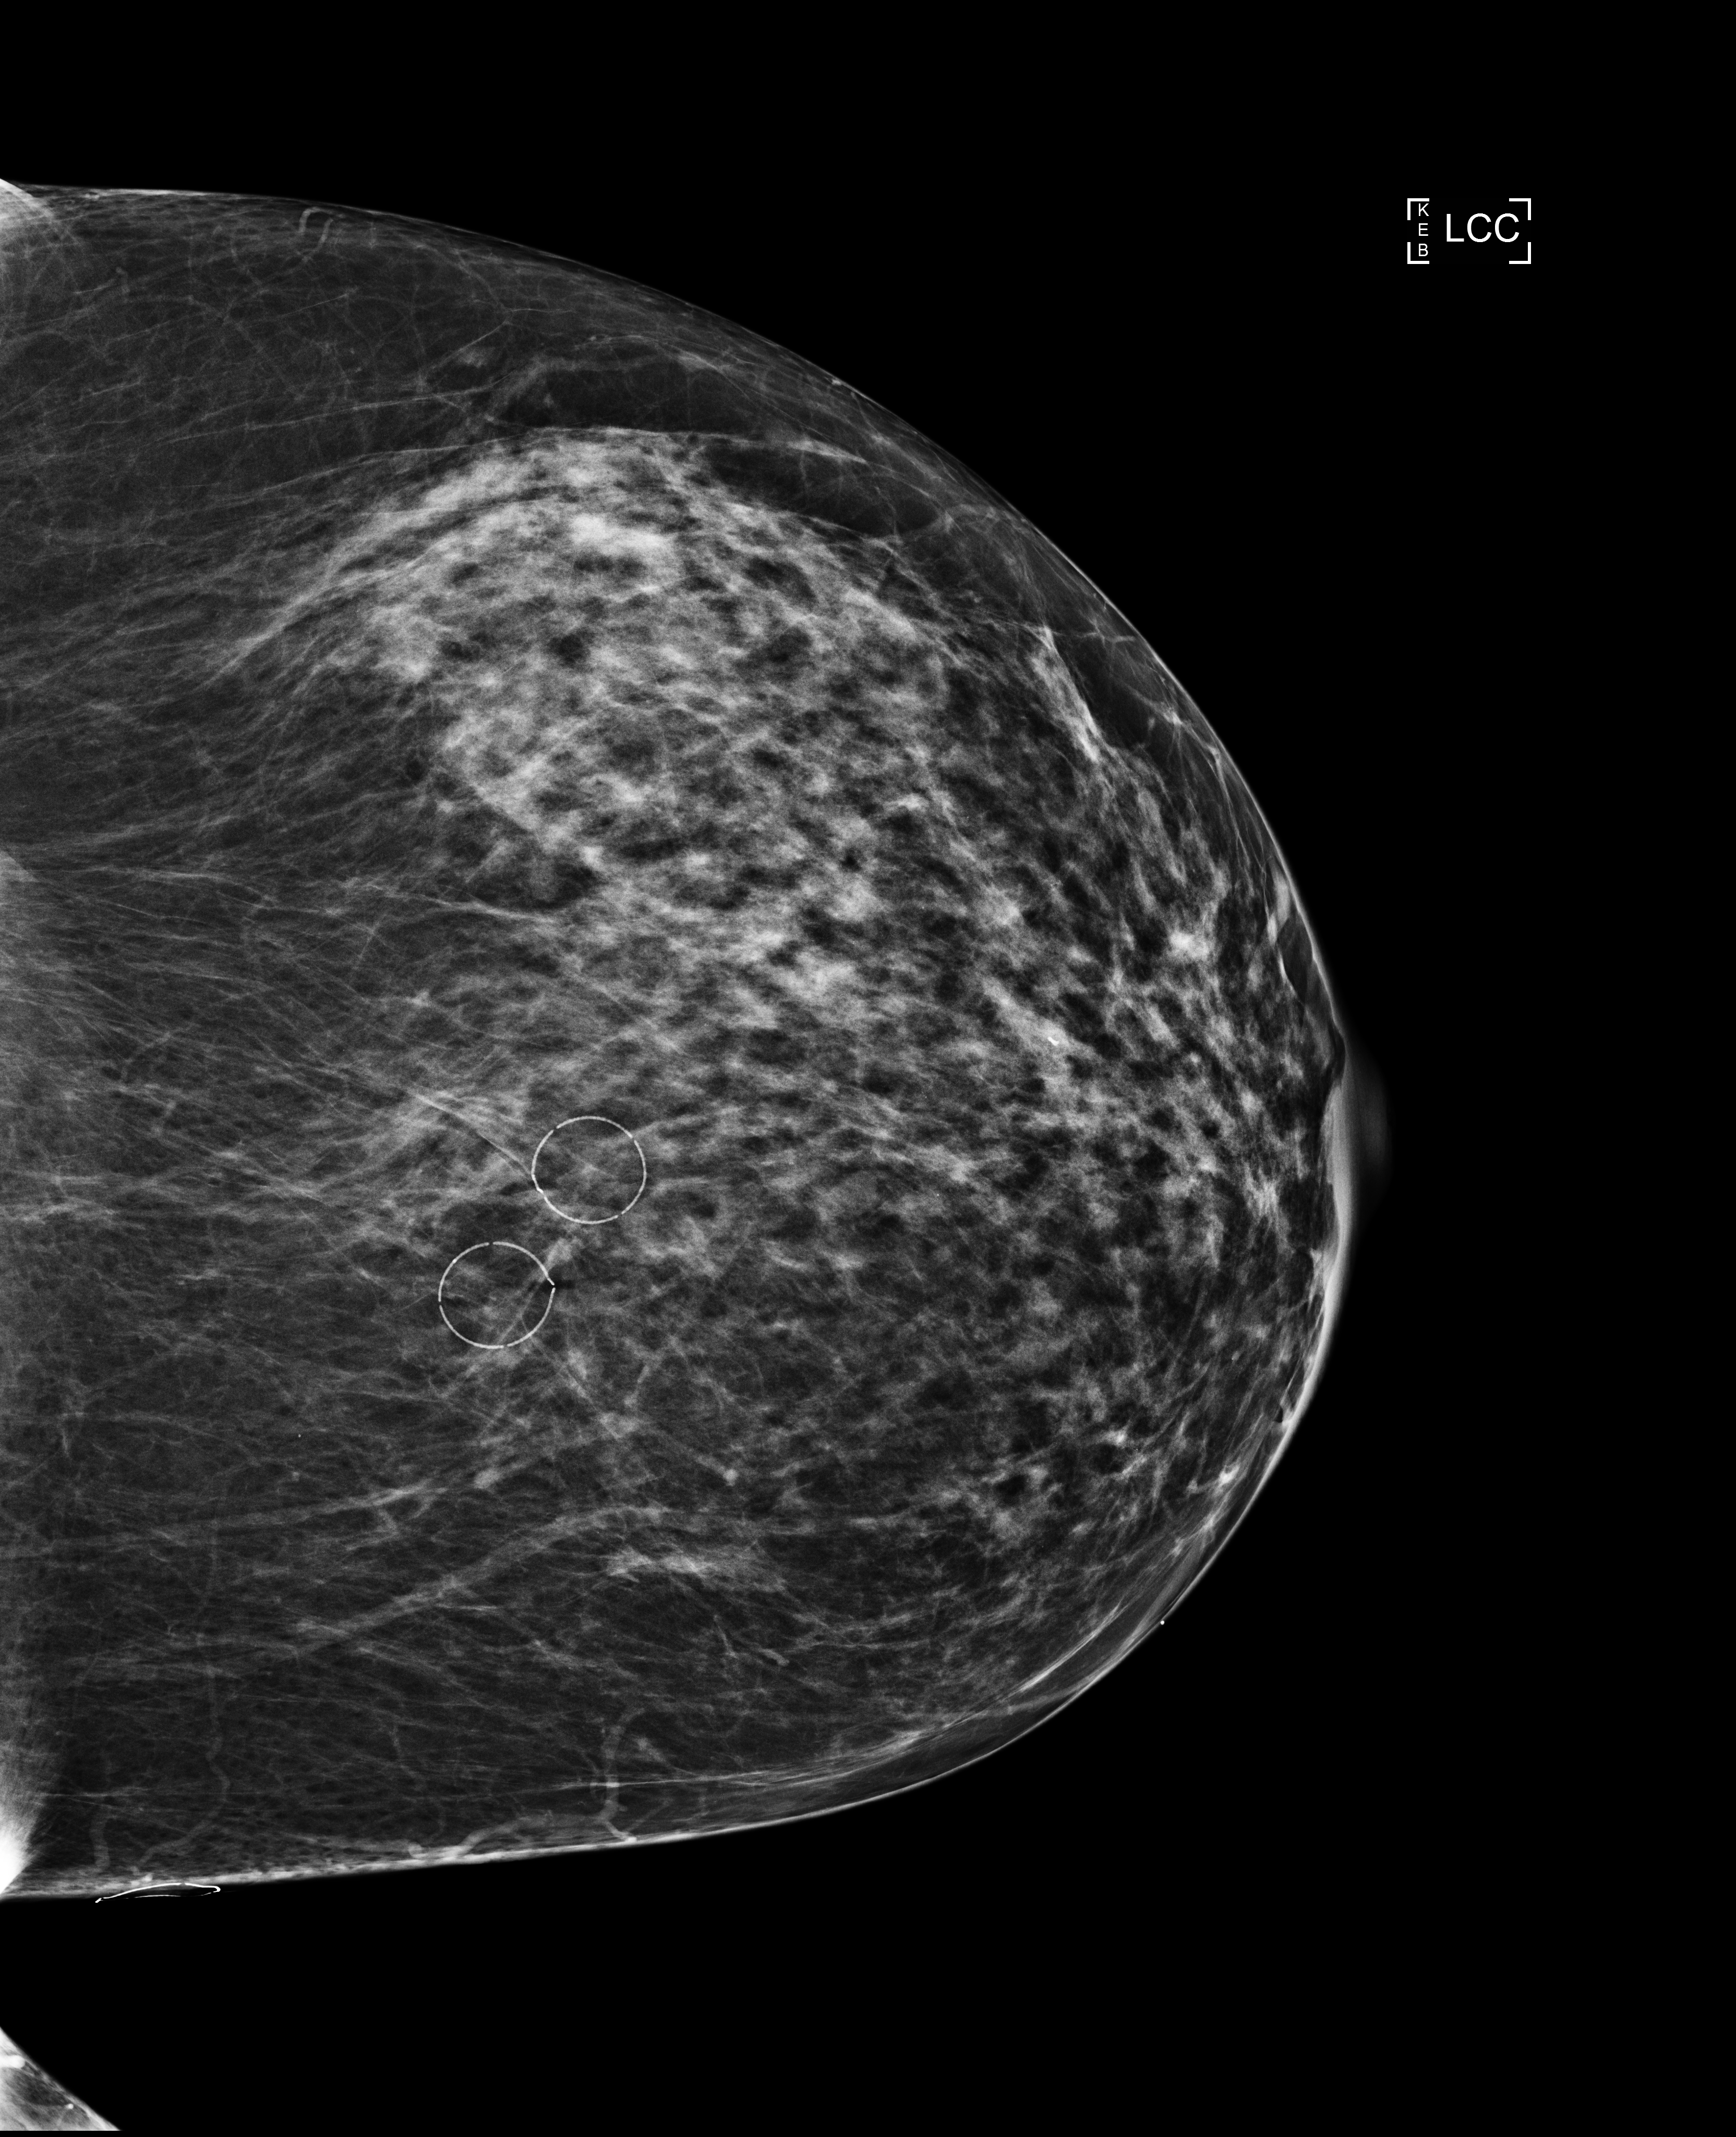
Annual screening mammography examination. Patient: female, 62 years.
Image type: full-field digital mammogram. Breast: left. Projection: cranio-caudal projection.